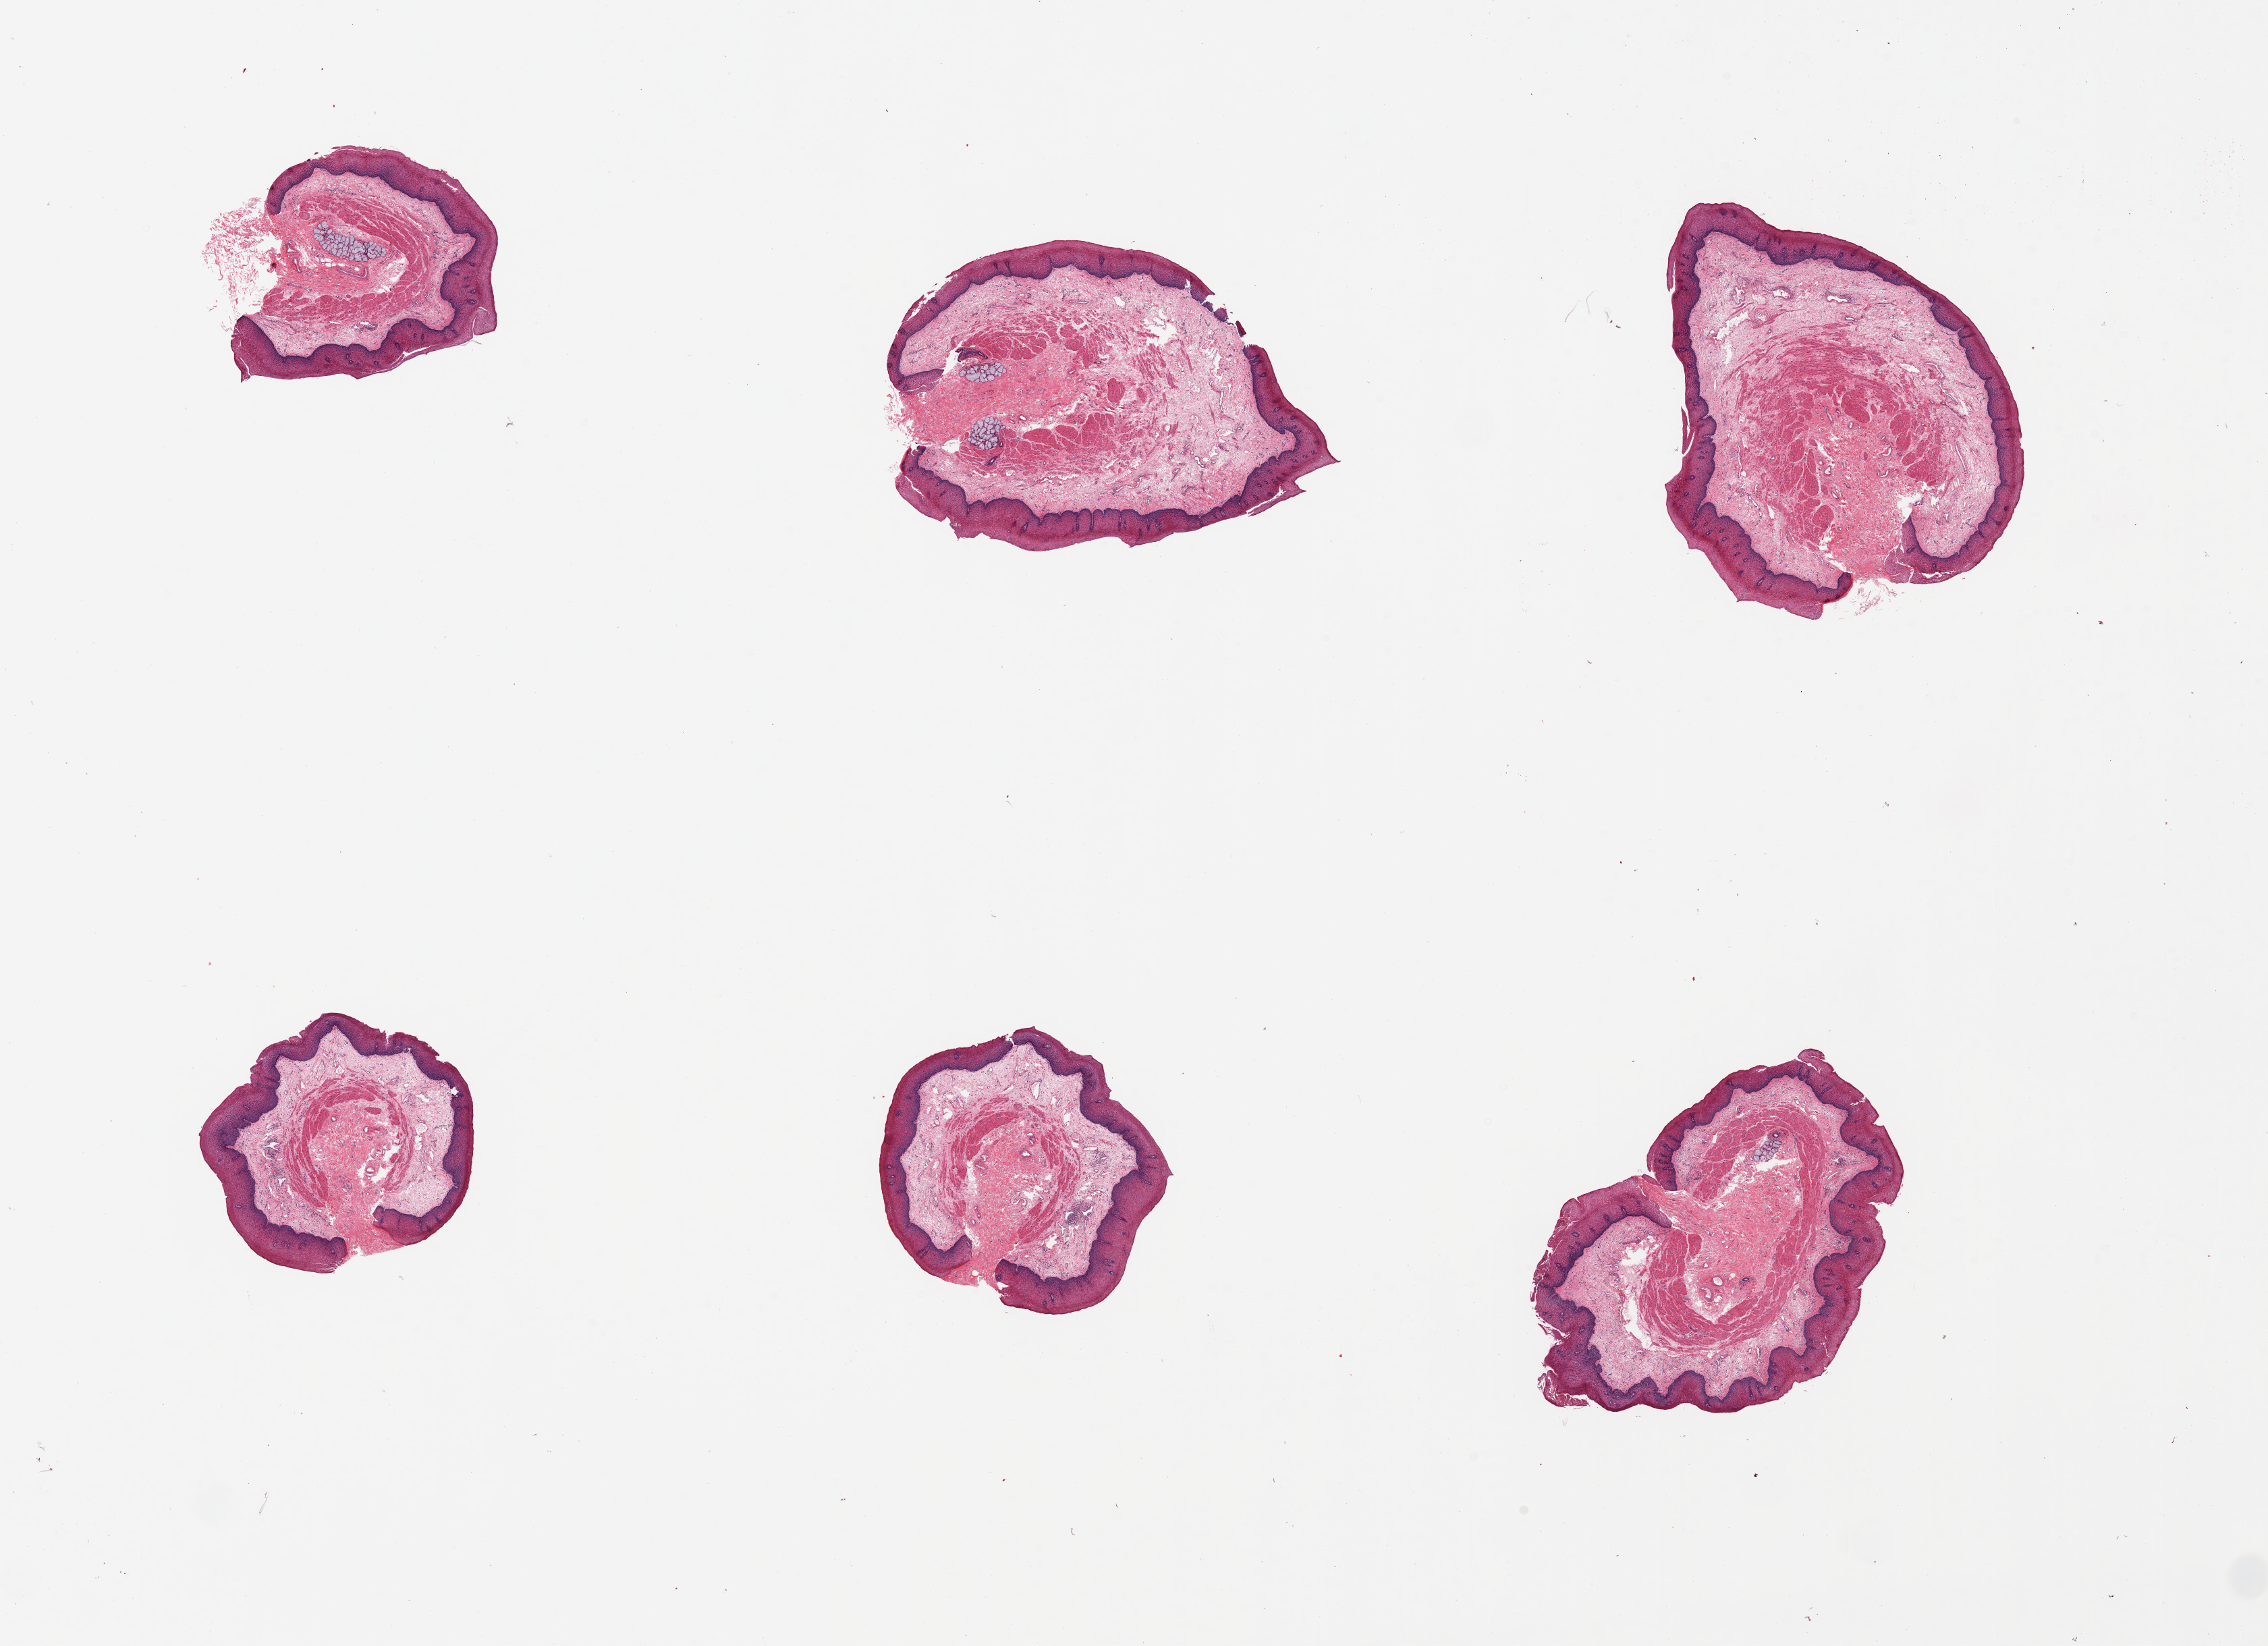
Whole-slide image, hematoxylin and eosin (H&E) stain, brightfield, a low-resolution overview of the entire scanned area, about 26.6 x 19.3 mm; PAXgene-fixed, paraffin-embedded tissue; target tissue: esophageal mucous membrane; tissue donor sample. Donor sex: male.
• review note (as recorded): 6 pieces, all contain squamous mucosa, ~10-20% thickness; Few submucosal mucus glands present